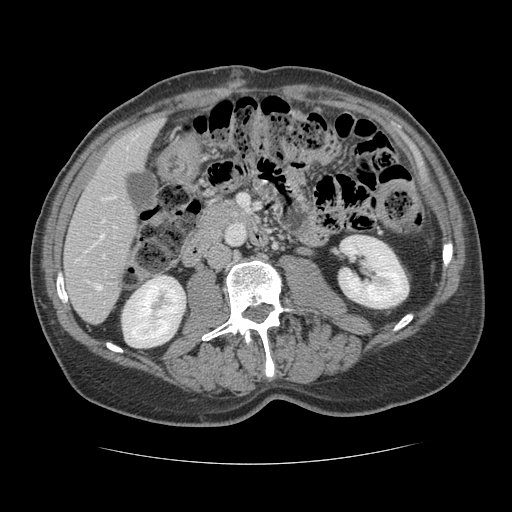
Contrast-enhanced abdominal CT, one axial slice. Slice 47 of 134 in the series (ordered by position). Reconstruction kernel STANDARD. 120 kVp. Soft-tissue window (W 400 / L 40 HU). 2.5 mm slice thickness. 512 × 512 image matrix, field of view 377 × 377 mm. Male patient, age 68 years. From the clinical record (not read from this slice): diagnosis: colorectal cancer liver metastases, imaged before liver resection.
Annotated regions visible in this slice (expert manual segmentation):
- hepatic veins: bounding box <100,196,116,238> (left, top, right, bottom; pixels)
- liver: <65,118,163,323>
- planned liver remnant (the part of the liver to remain after resection): <65,118,163,323>
- portal vein (with intrahepatic branches): <95,255,105,290>